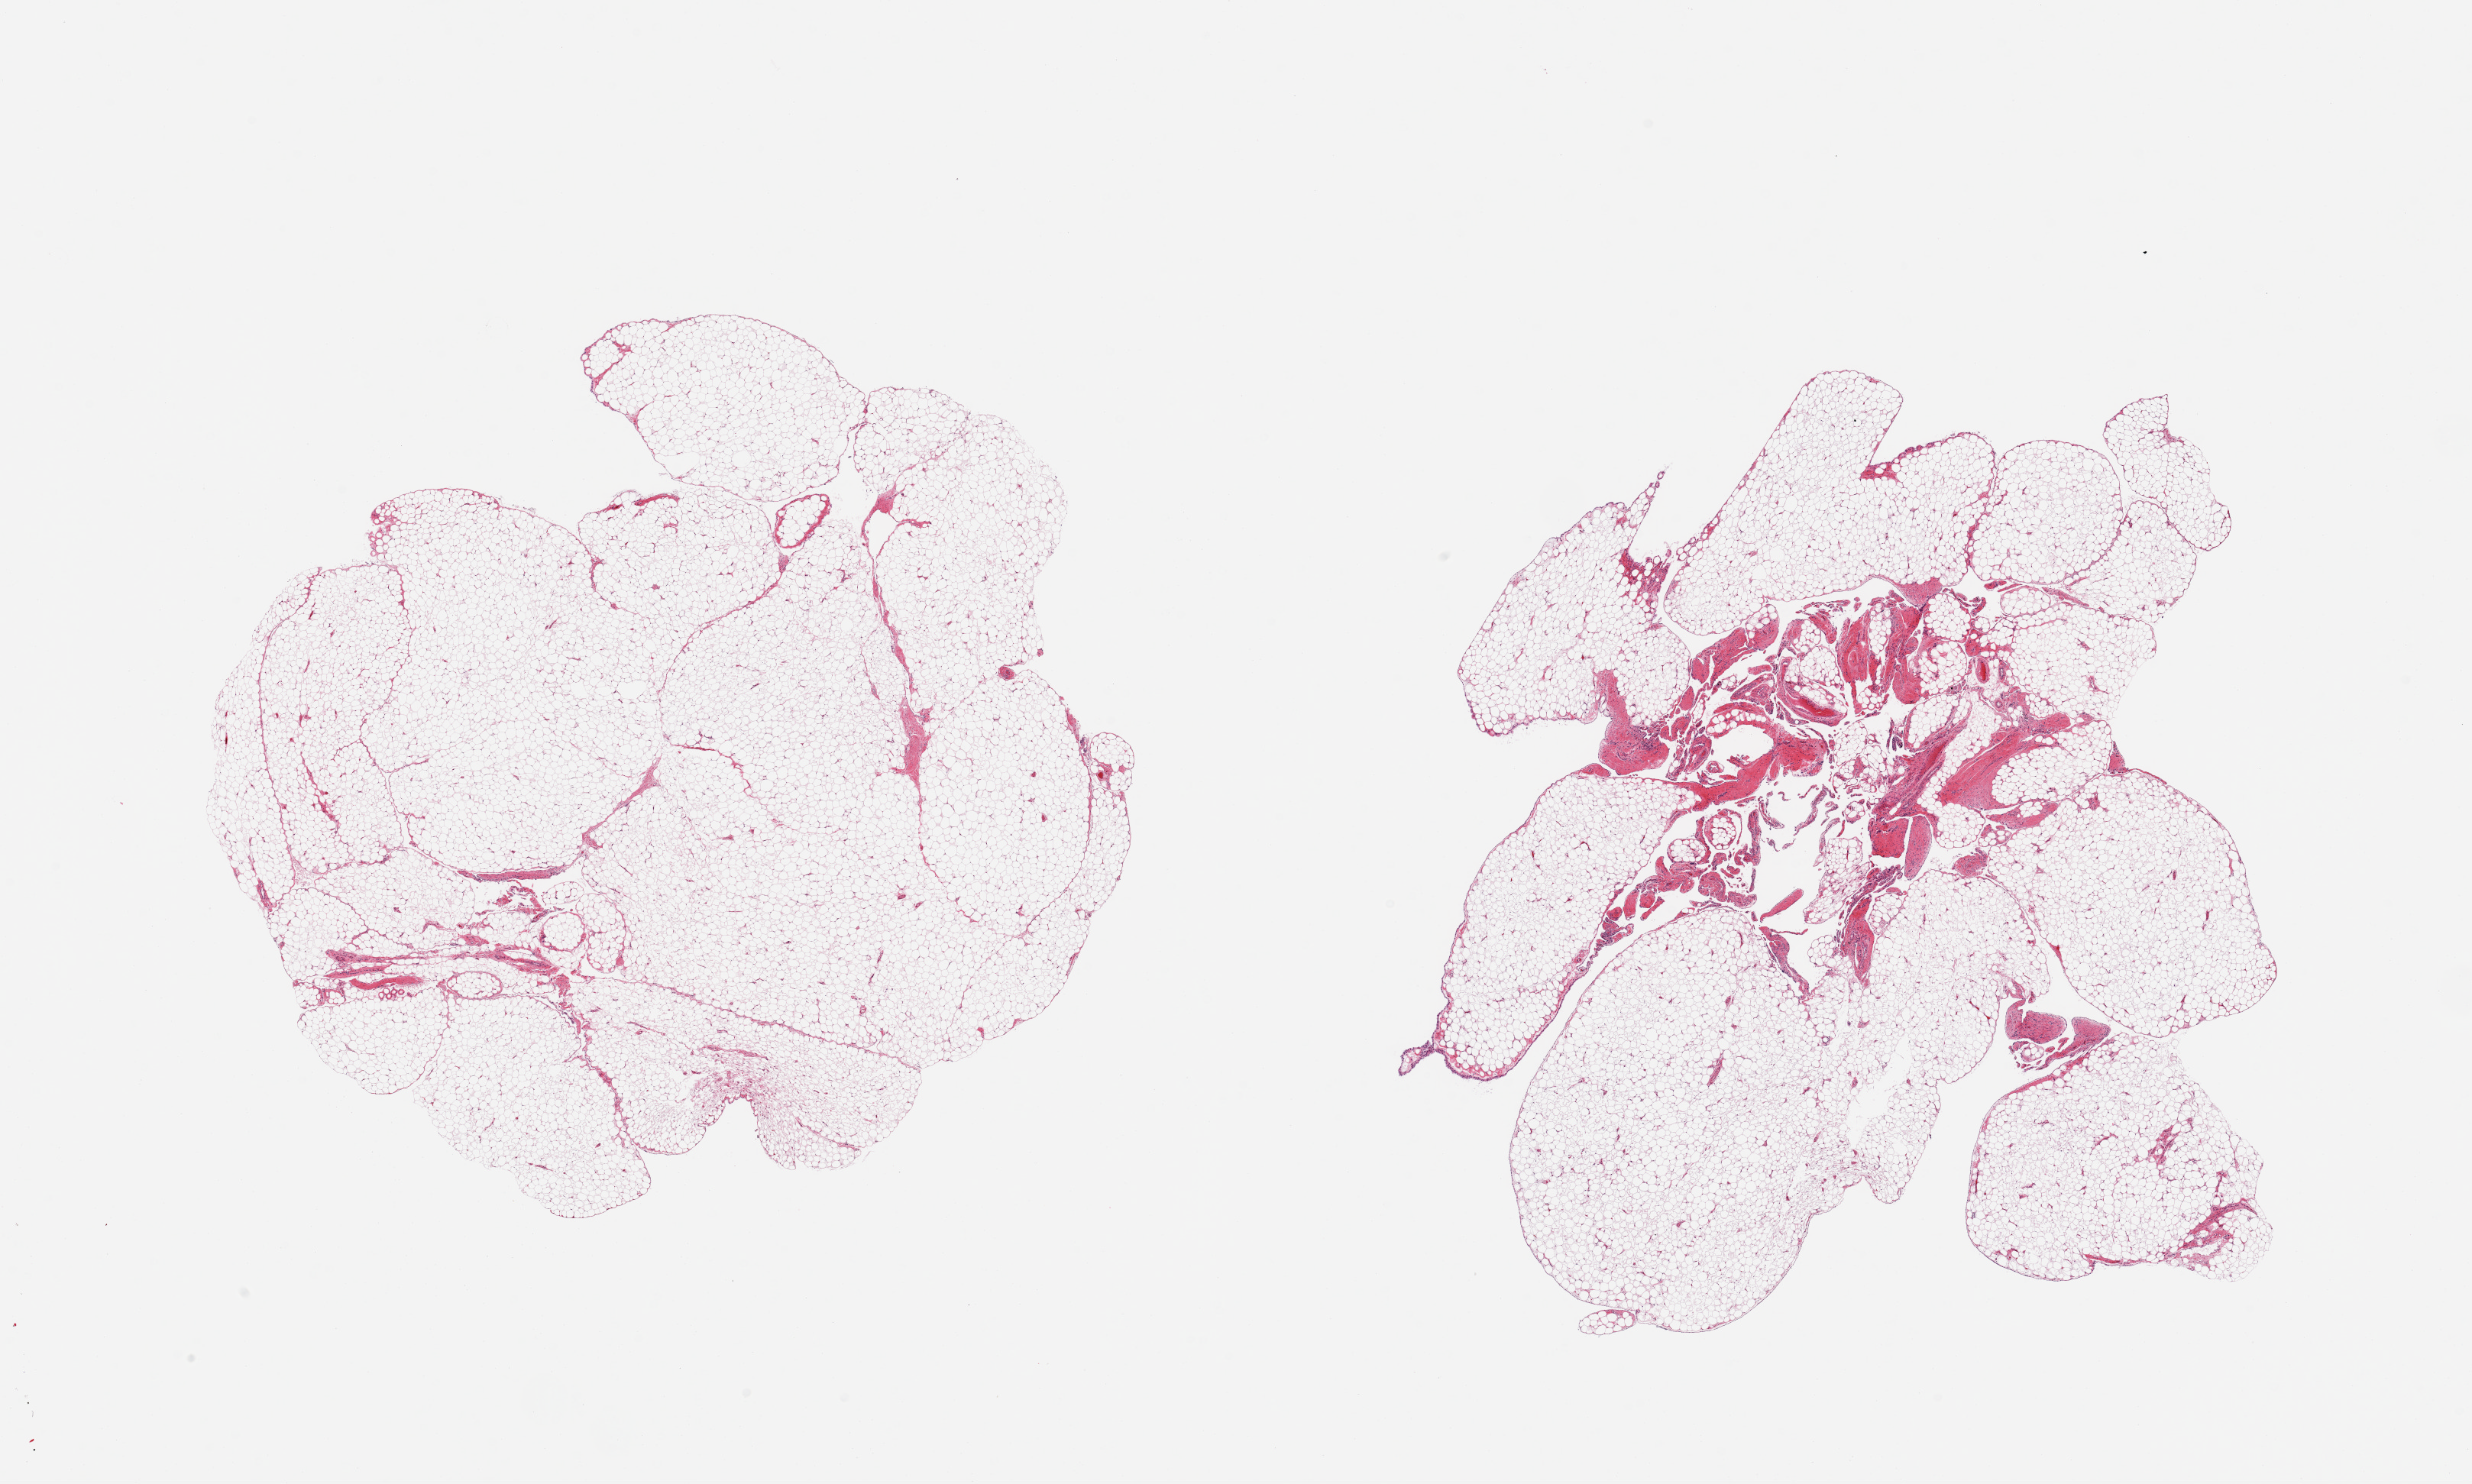
Hematoxylin and eosin (H&E) whole-slide image, low-resolution overview of the scanned area, about 25.6 x 15.4 mm; PAXgene-fixed, paraffin-embedded tissue; section of omentum (target tissue); donor tissue sample. Male donor.
Reviewer comment on this tissue sample: 2 pieces; 10% fibrous content in 1 piece.